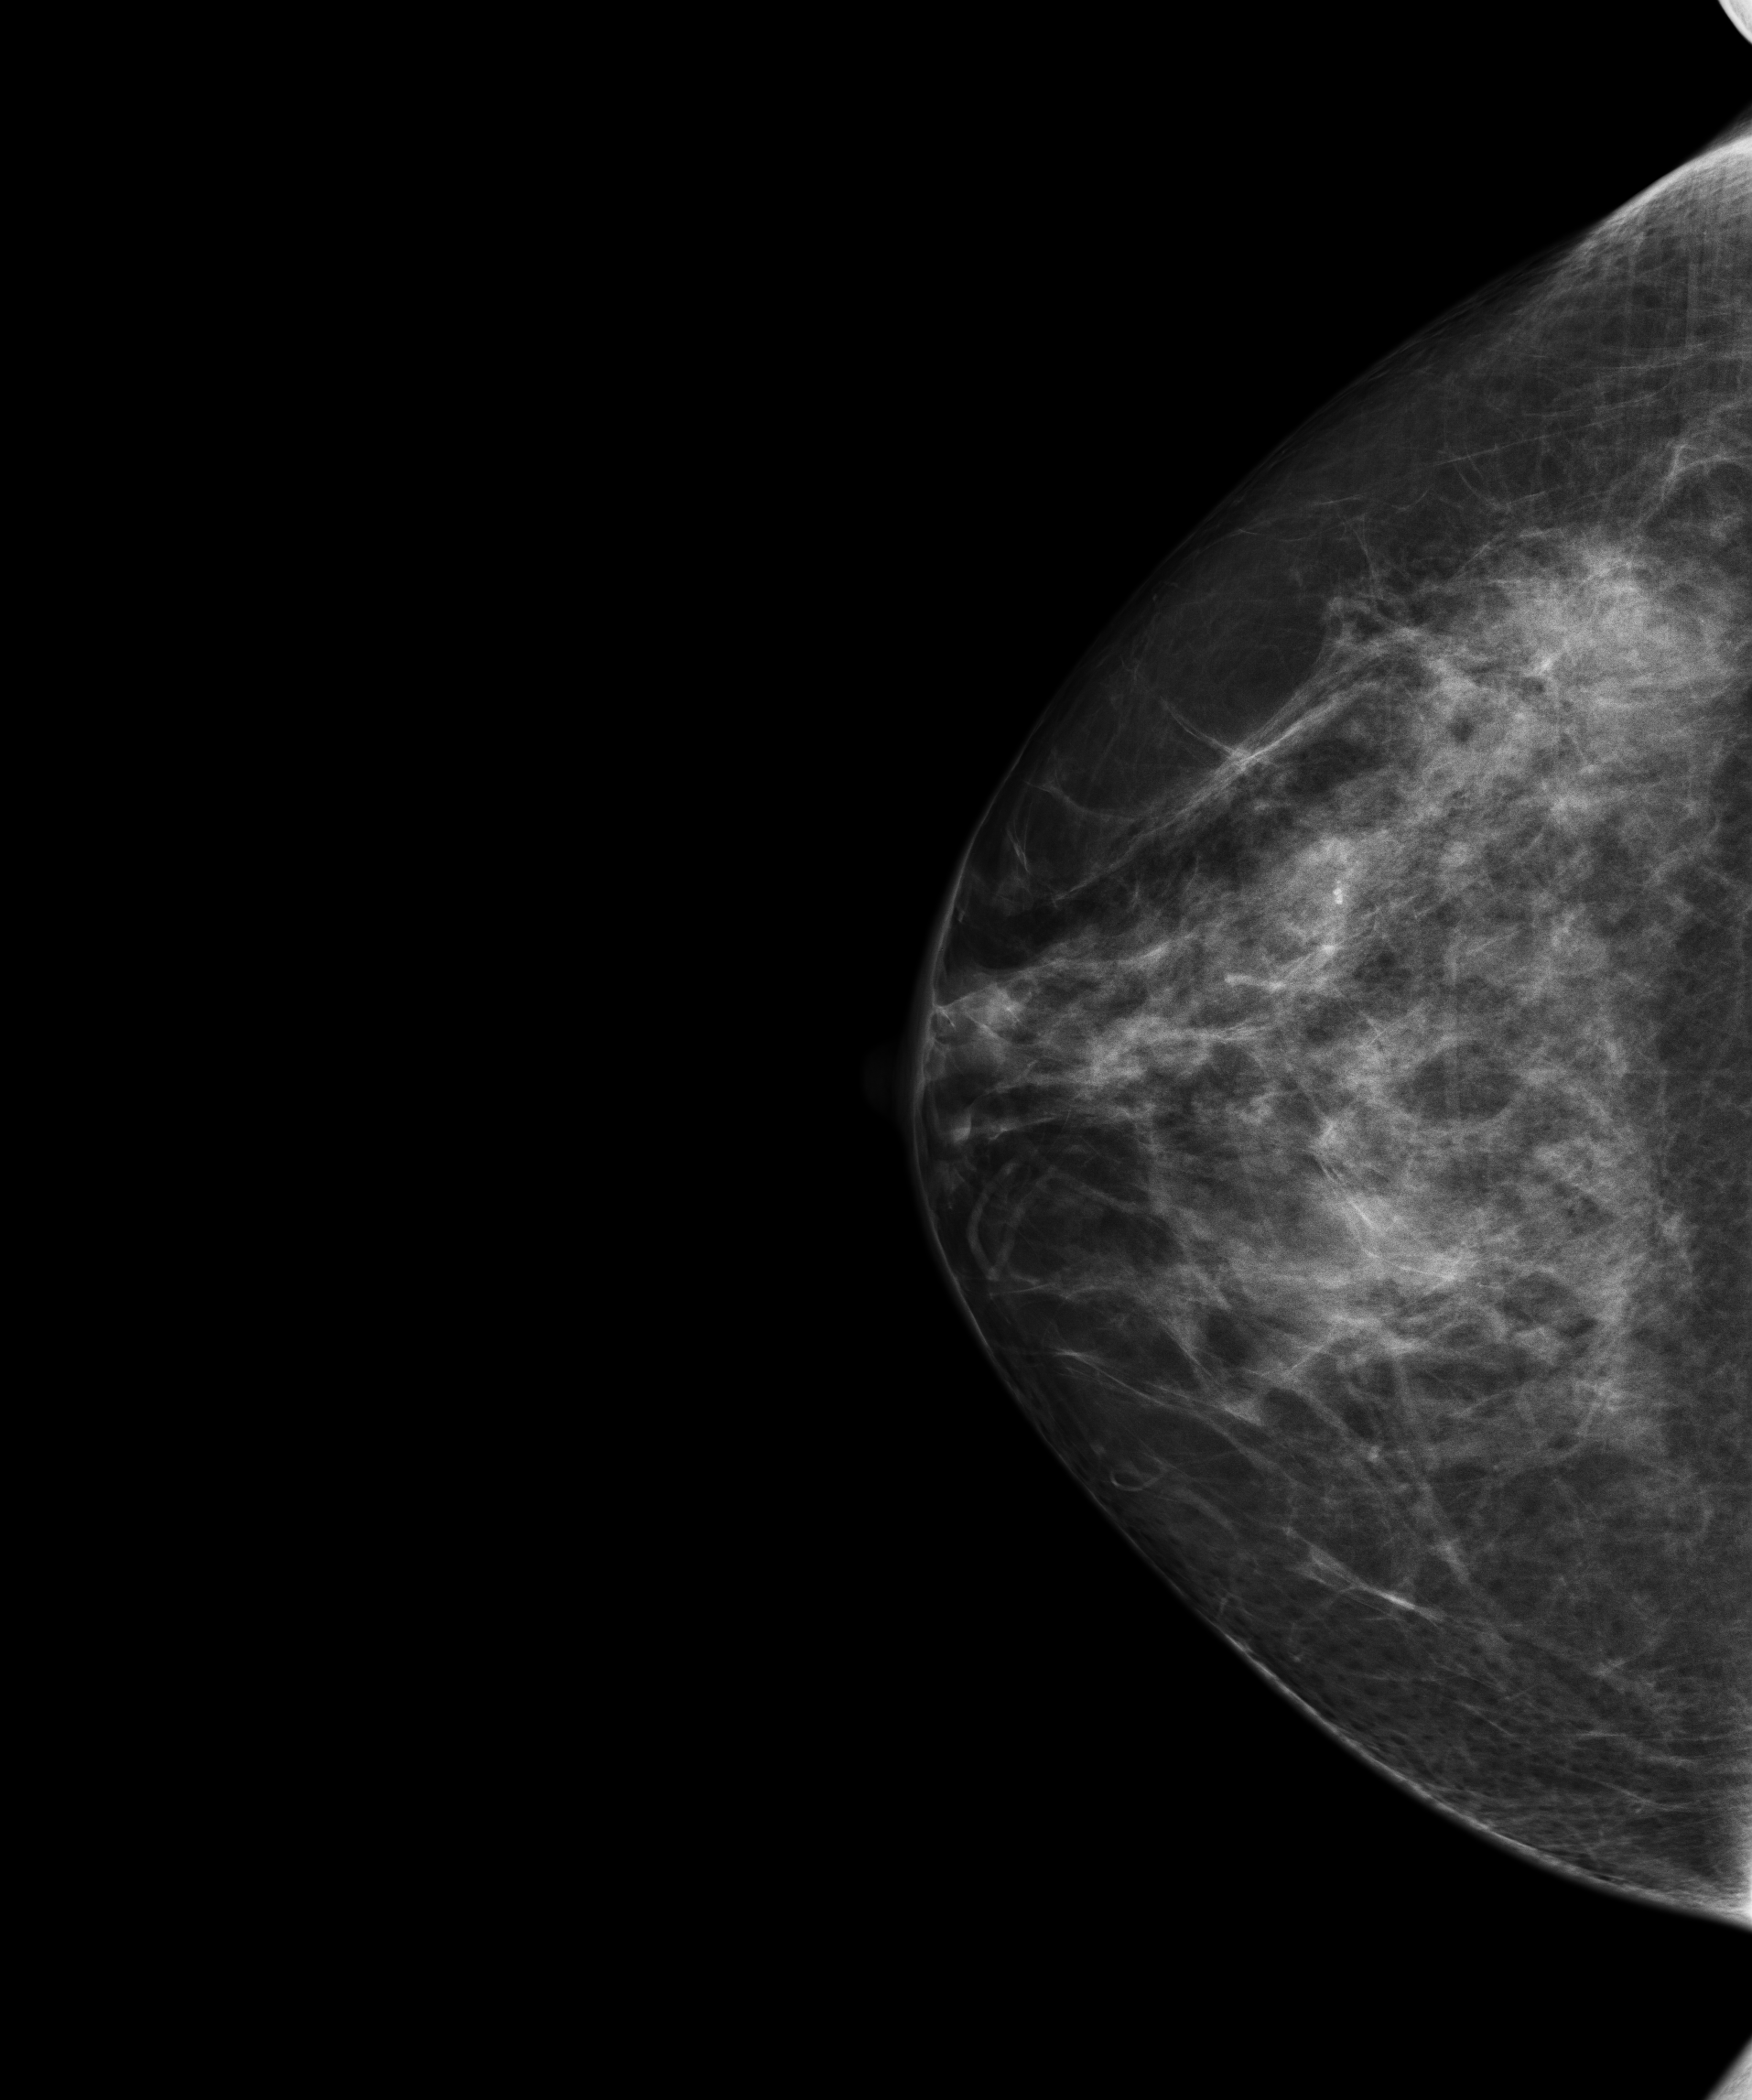
Digital mammogram (FFDM), right breast, cranio-caudal projection, annual screening mammography examination. Patient: female, 45 years.
BI-RADS breast density category at the screening exam (both breasts, scale 1–4): 3. Final BI-RADS assessment for this screening round (tomosynthesis exam, both breasts): category 1. Recall: no recall after this screen.